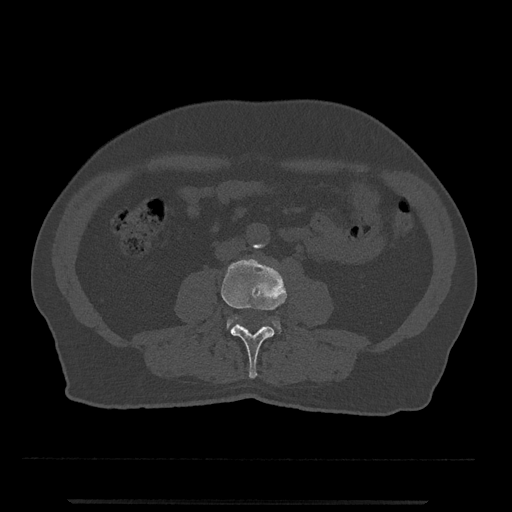
CT including the spine, one axial slice; position 185 of 797 along the scan axis; reconstruction kernel Br40s/3; bone window (W 1800 / L 400 HU); 0.5 mm slice thickness; 512 × 512 image matrix, field of view 419 × 419 mm. Male patient, age 63 years. Case-level facts recorded for this patient, not image findings: primary cancer: prostate.
Annotated regions visible in this slice (semi-automatic segmentation, software-assisted and operator-edited):
- L3 vertebra: bounding box [x1, y1, x2, y2] px = [221, 259, 287, 379]
- L4 vertebra: [227, 317, 281, 332]